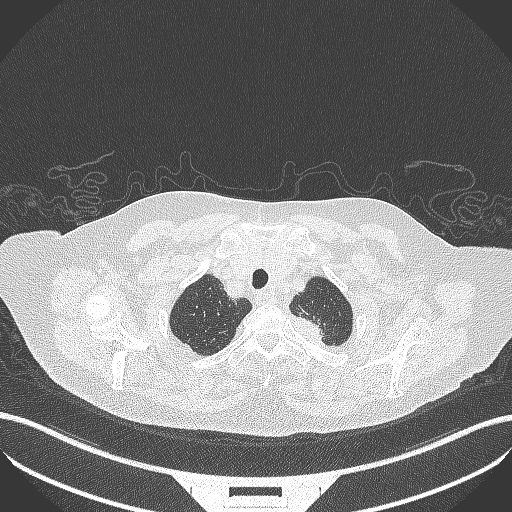
Chest CT, one axial slice; slice 311 of 353 in the series (ordered by position); reconstruction kernel B70f; 100 kVp; lung window (W 1500 / L -600 HU); 1 mm slice thickness; 512 × 512 image matrix. Patient: female, 81 years. Case-level facts recorded for this patient, not image findings: clinical TNM (as recorded): T2a N0 M0.
Annotated regions visible in this slice (rectangle marked by the reading radiologist):
- lung tumour (recorded histology: adenocarcinoma): bounding box [x1, y1, x2, y2] px = [295, 311, 334, 356]